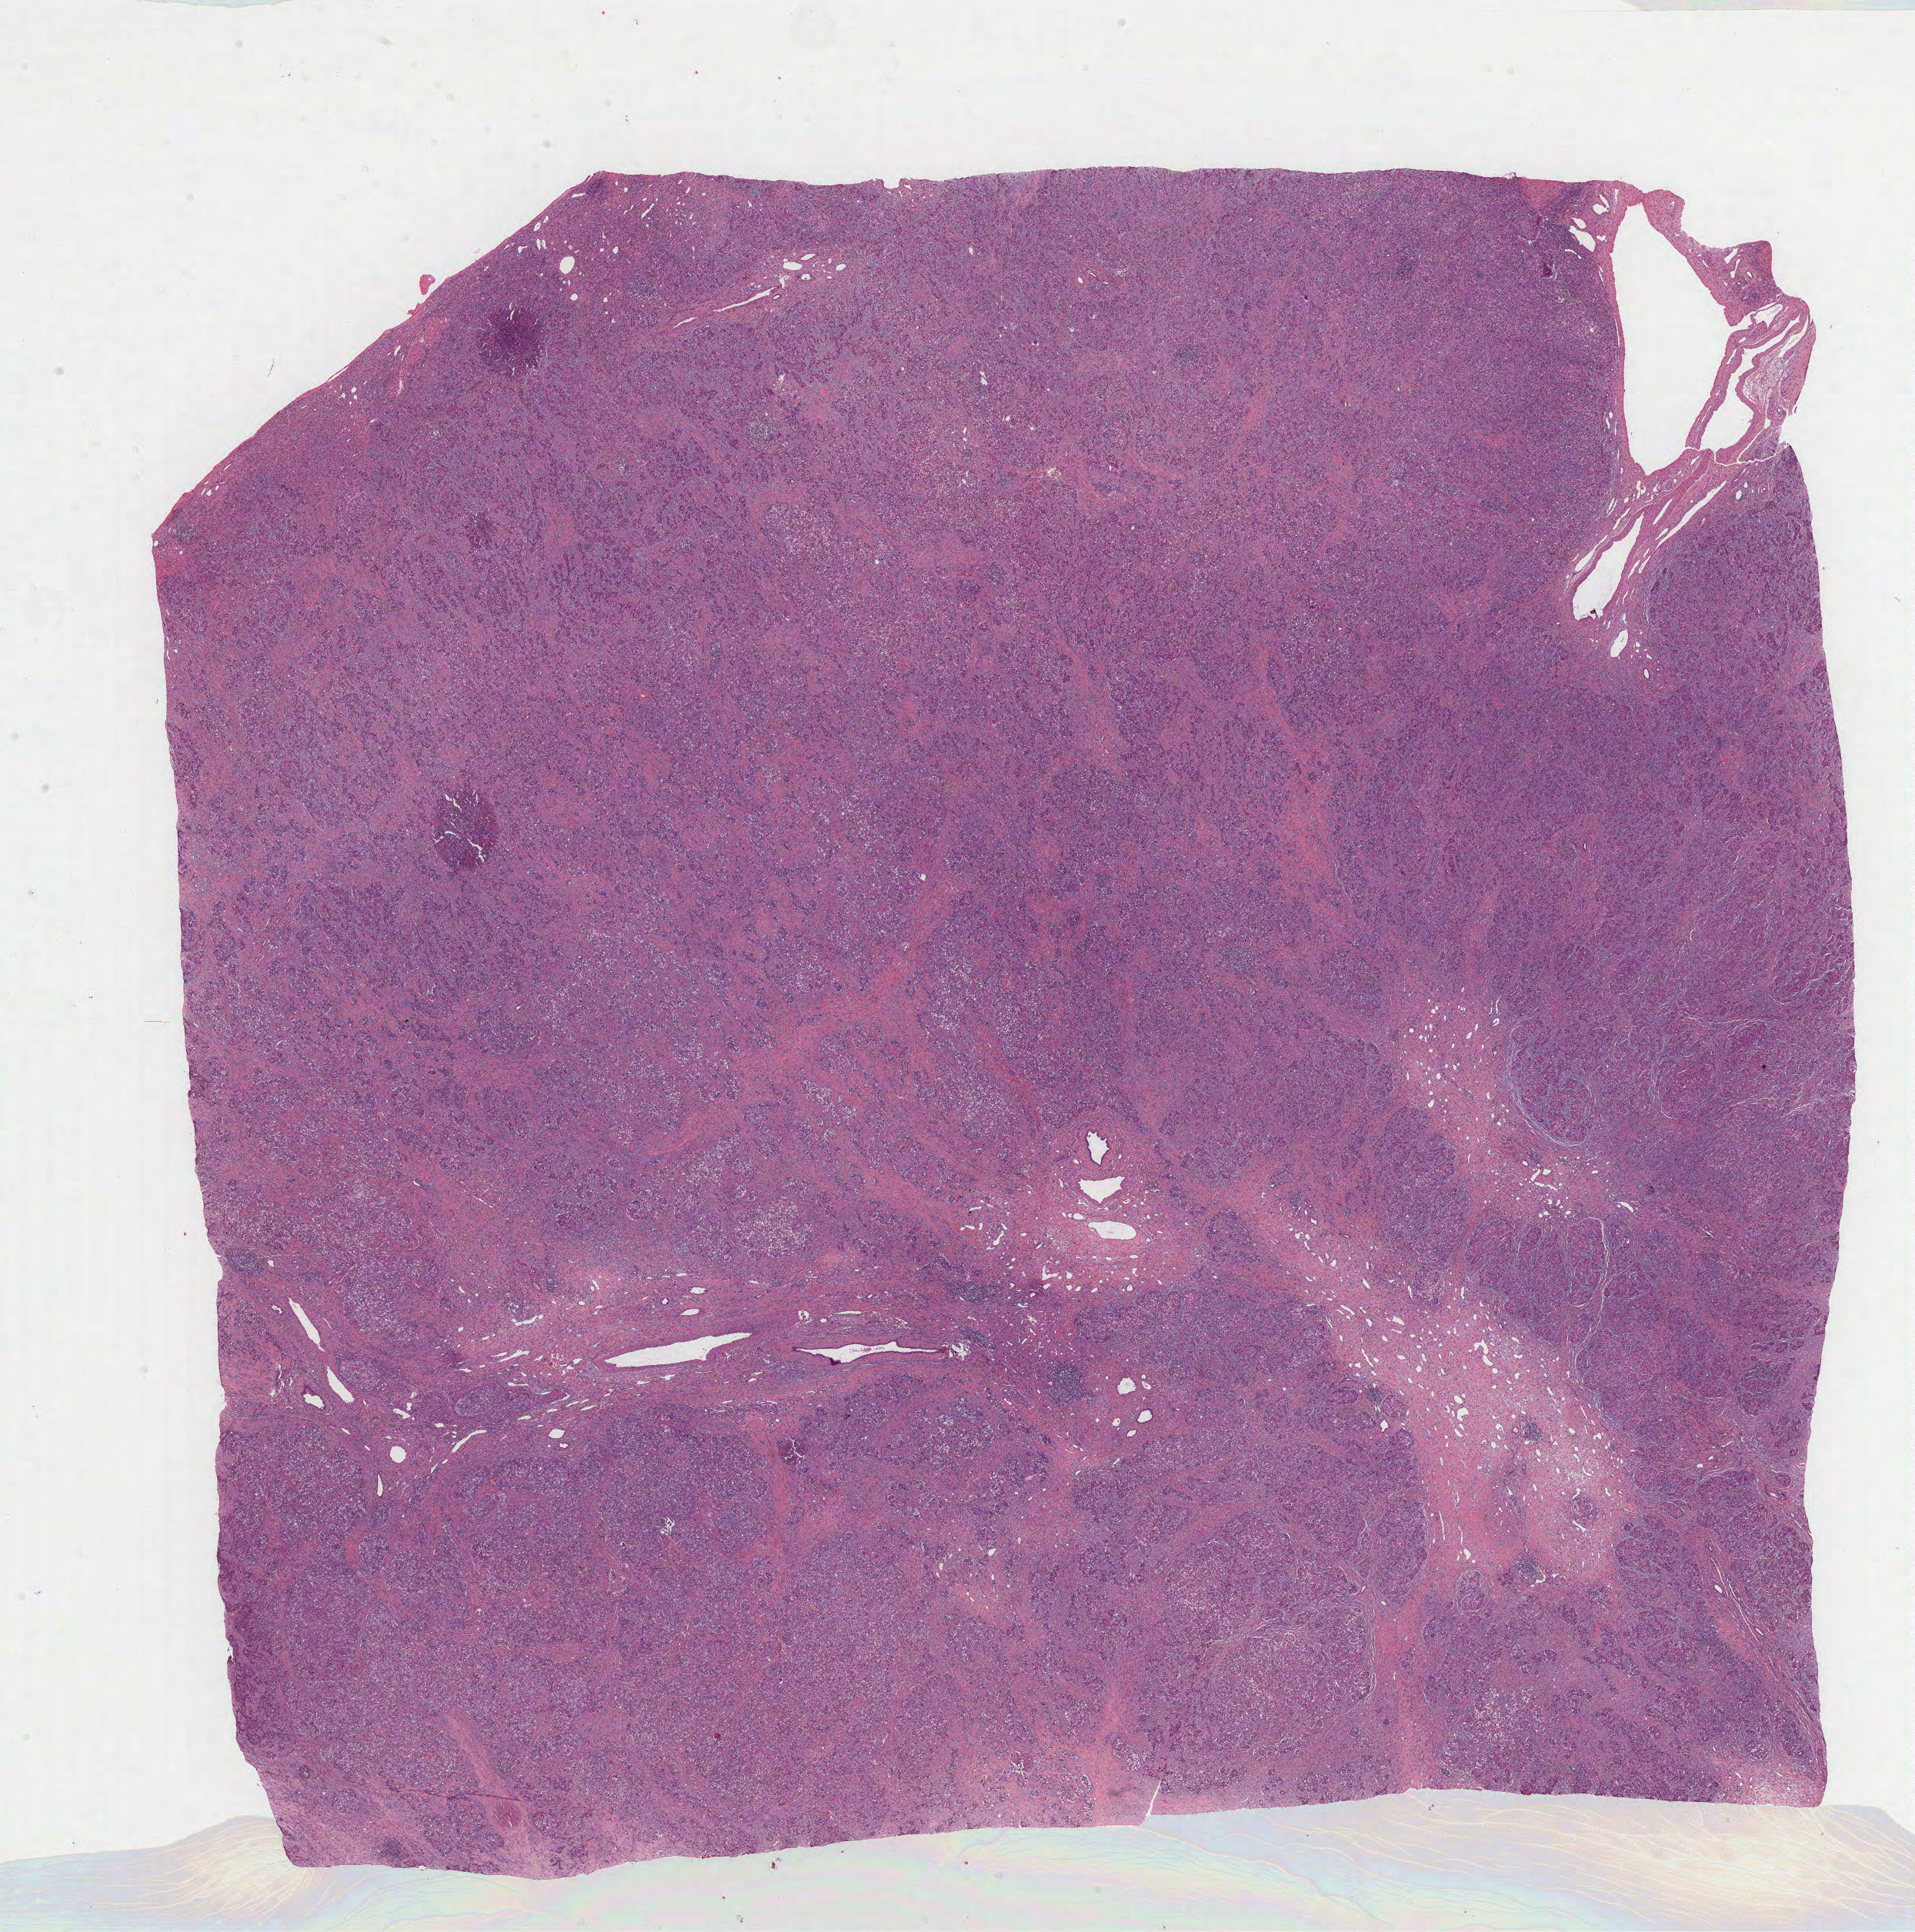
Whole-slide histology image, H&E-stained — a low-resolution overview of the entire scanned area, about 20.1 x 20.3 mm (acquisition: 40x scan), formalin-fixed paraffin-embedded (FFPE) diagnostic section, sample: primary tumour, liver. Patient: female, age at initial diagnosis 59 years.
Histologic diagnosis: Hepatocellular carcinoma, NOS.